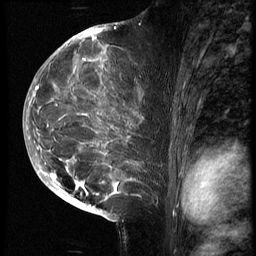
Breast MRI (dynamic contrast-enhanced), one sagittal slice. Slice 36 of 70 in the series (ordered by position). 3 images stored at this slice position (order not interpretable as contrast timing). 1.5 T. TE 4.2 ms, TR 9 ms. 256 × 256 image matrix, field of view 180 × 180 mm. Patient: female, 28 years. From the clinical record (not read from this slice): setting: breast cancer imaged before/during neoadjuvant chemotherapy.
Outlined on this slice (semi-automatic segmentation, software-assisted and operator-edited):
- analysis volume of interest (the breast-tissue region the enhancement analysis was run in; not a lesion): box from (x=43, y=42) to (x=163, y=215) px
- tumour enhancement mask (voxels above the 140 % enhancement threshold inside the analysis volume of interest): (x=46, y=42)–(x=134, y=201)